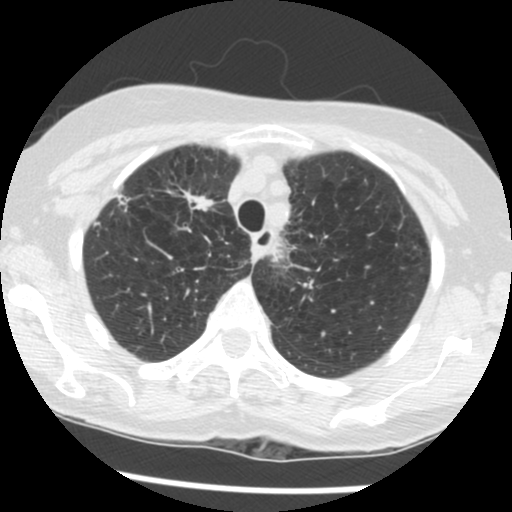
Low-dose screening chest CT, axial slice; second screening round (one year after baseline); lung window (W 1500 / L -600 HU); 2.5 mm slice thickness; 120 kVp. Female participant, aged 70 years at enrolment. Former smoker at enrolment.
Expert reader's lesion annotation, bounding box (x1, y1, x2, y2) in pixels: (157, 173, 224, 228). The exam's reader record, not a measurement of the box and not confirmed to be the same lesion: non-calcified nodule or mass ≥4 mm, right upper lobe, 11 × 7 mm, spiculated (stellate) margins, soft tissue attenuation, pre-existing on the prior screen: yes; interval growth: yes. Later outcome: lung cancer diagnosed 248 days after this screen — non-small cell carcinoma, right upper lobe, stage IV (AJCC 6th edition), 30 mm at pathology.